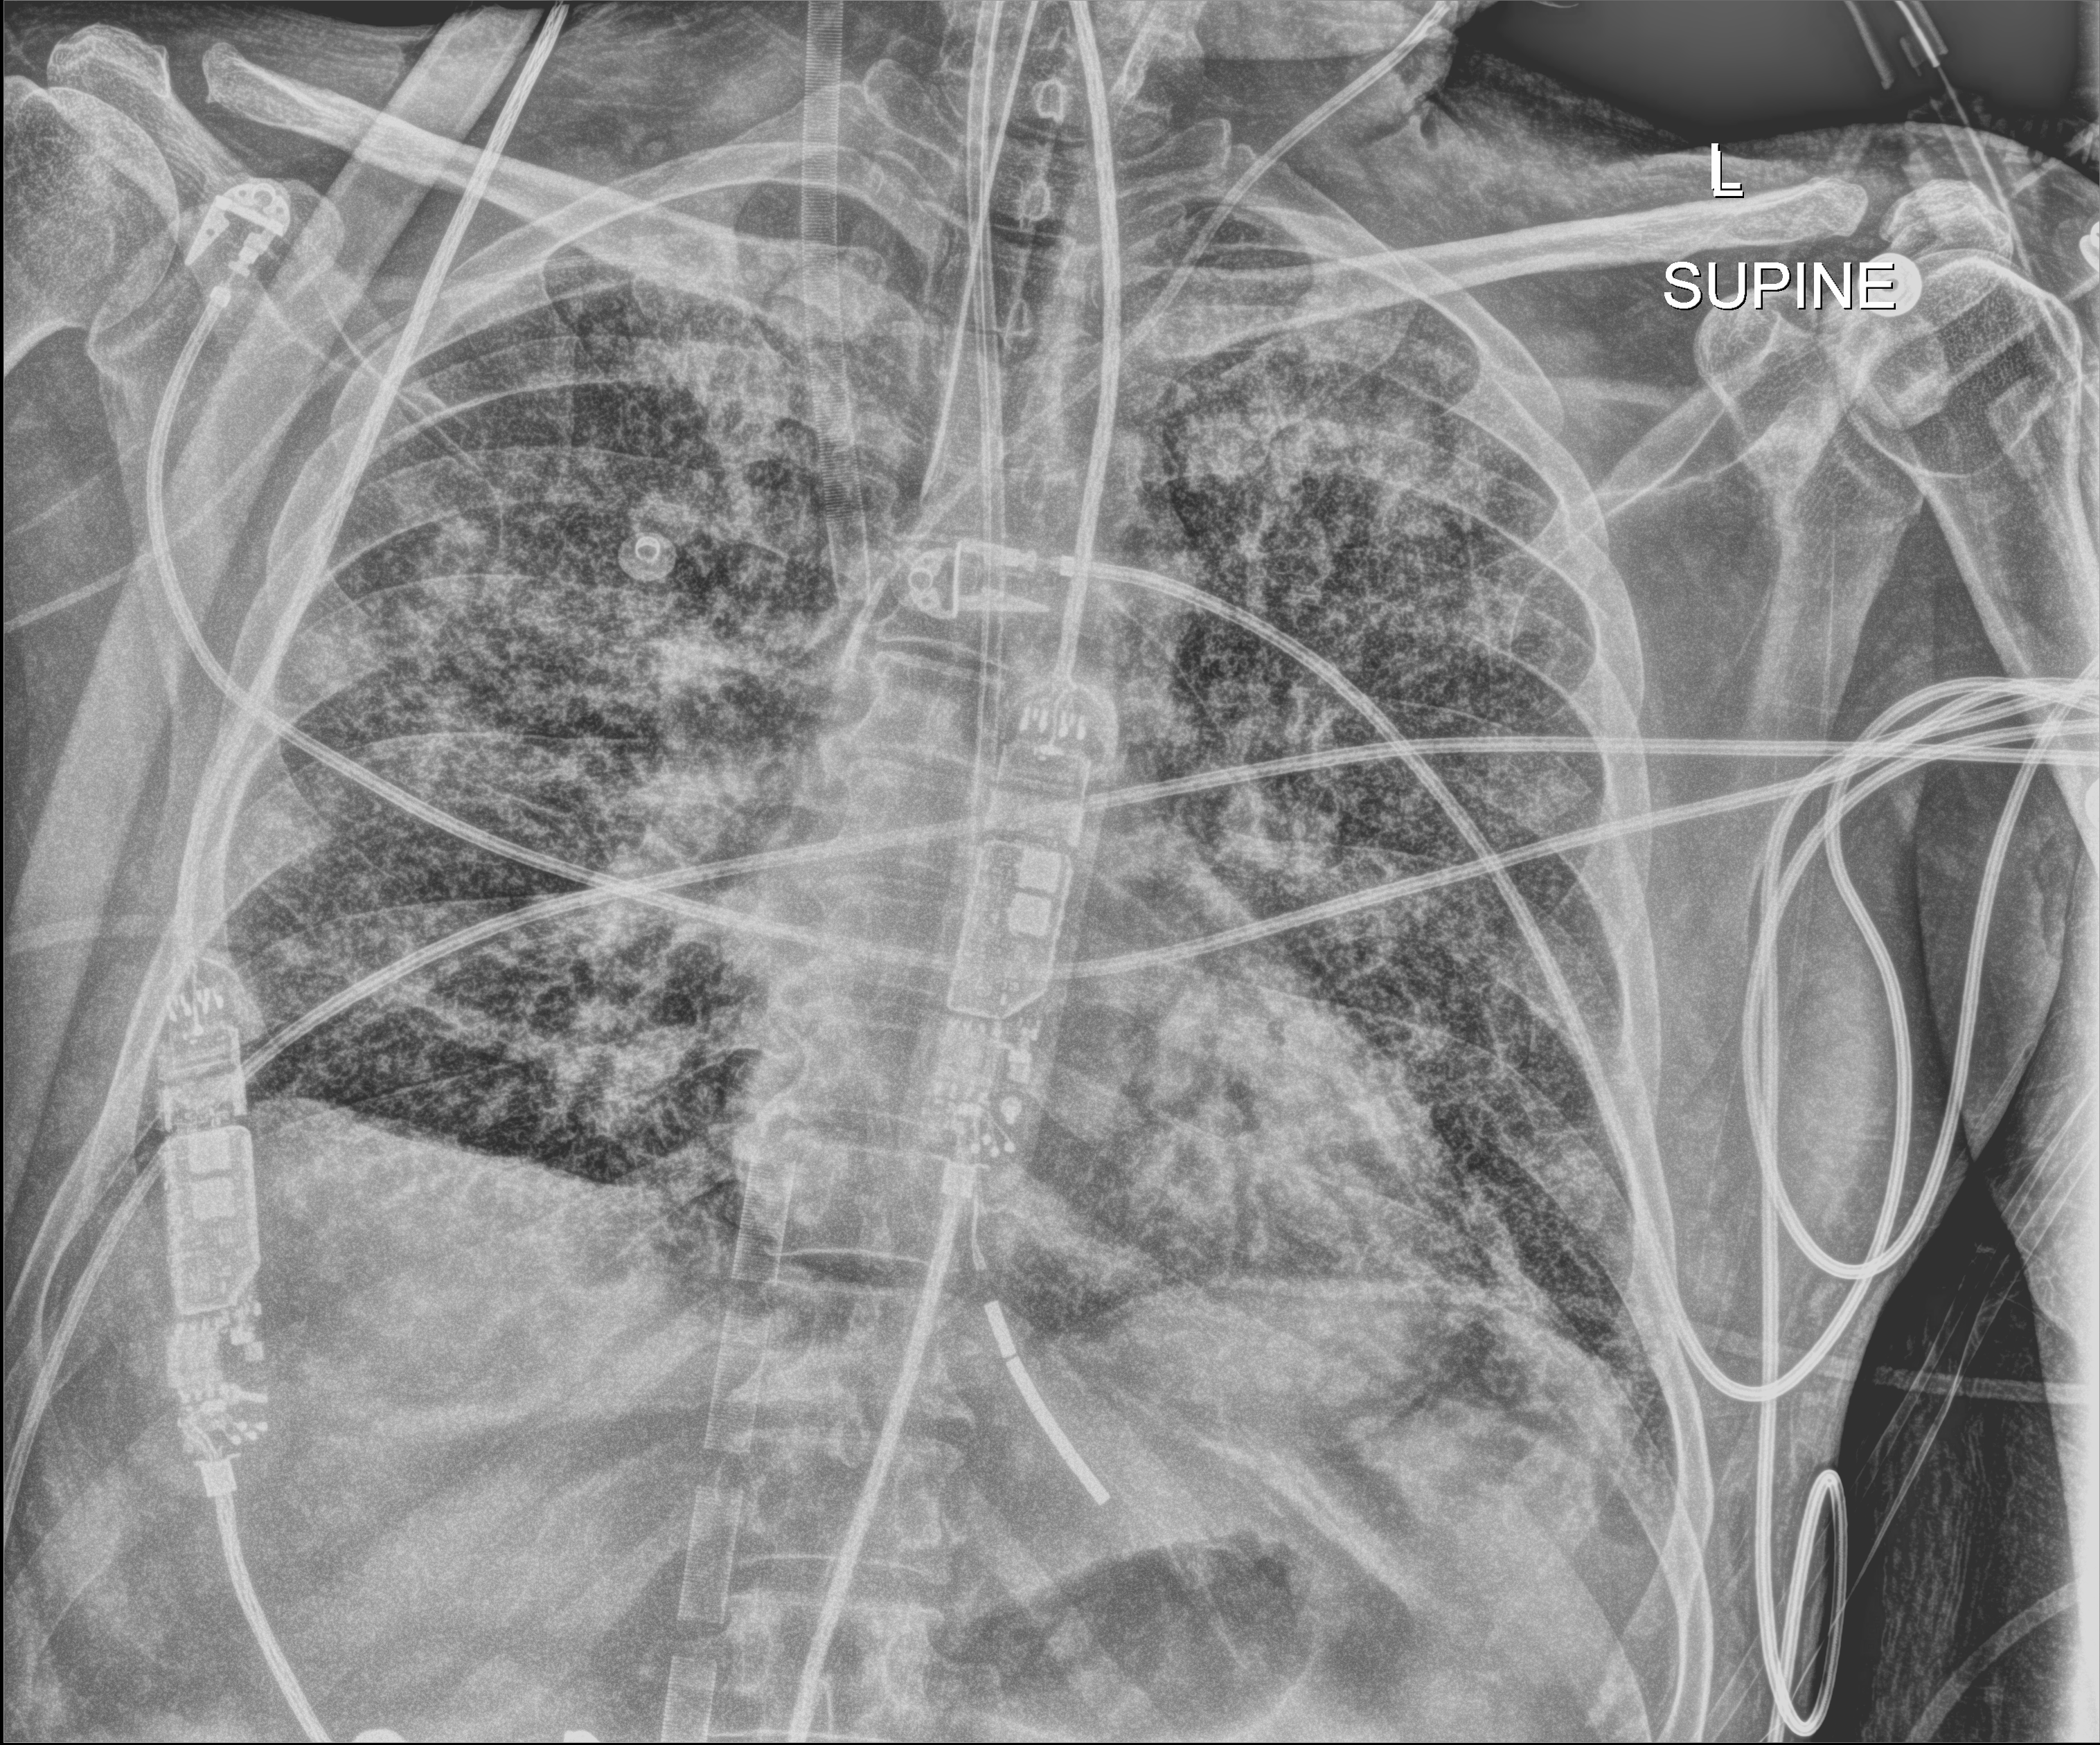
Bedside chest radiograph (digital radiography); anteroposterior (AP) projection. Patient hospitalised with COVID-19; male, aged 18–59 years.
Admission-level facts for this patient (not findings on this image; timing relative to this image not recorded): smoking status (admission record): never.